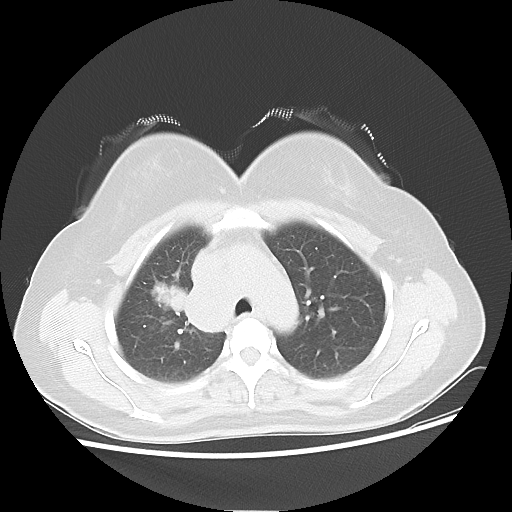
Chest CT, one axial slice. Slice 37 of 50 in the series (ordered by position). Reconstruction kernel LUNG. 100 kVp. Lung window (W 1500 / L -600 HU). 512 × 512 image matrix, field of view 360 × 360 mm. Female patient, age 40 years. Case-level facts recorded for this patient, not image findings: clinical TNM (as recorded): T1c N3 M0; histopathological grade: G3.
Annotated regions visible in this slice (bounding box drawn by a radiologist):
- lung tumour (recorded histology: small cell carcinoma): bounding box (x1, y1, x2, y2) in pixels: (147, 275, 191, 329)